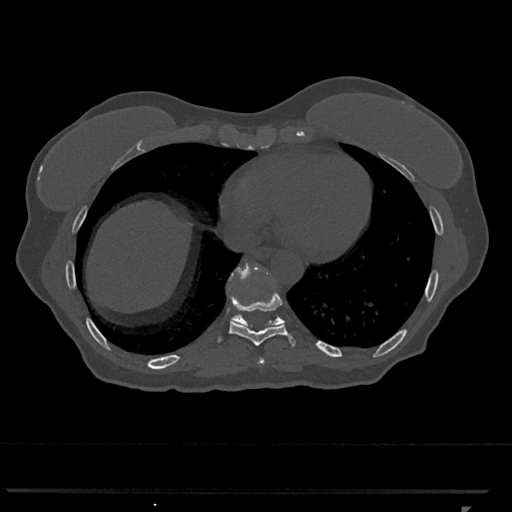
CT including the spine, one axial slice. Slice 608 of 793 in the series (ordered by position). Reconstruction kernel Br40s/3. 120 kVp. Bone window (W 1800 / L 400 HU). 512 × 512 image matrix, field of view 380 × 380 mm. Patient: female, 62 years. Case-level facts recorded for this patient, not image findings: primary cancer: renal.
Outlined on this slice (semi-automatic segmentation, software-assisted and operator-edited):
- T10 vertebra: bounding box (x1, y1, x2, y2) in pixels: (229, 263, 285, 328)
- T8 vertebra: (258, 357, 265, 364)
- T9 vertebra: (219, 293, 295, 346)